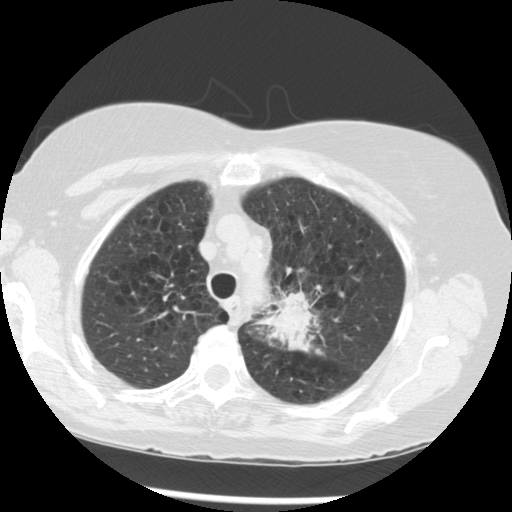
Low-dose screening chest CT, one axial slice; position 223 of 283 along the scan axis; 120 kVp; lung window (W 1500 / L -600 HU); 2.5 mm slice thickness; 512 × 512 image matrix, field of view 330 × 330 mm.
Structures marked on this image (manually delineated by an expert):
- lesion 1 (tumor, upper lobe of left lung): bounding box (x1, y1, x2, y2) in pixels: (251, 291, 322, 353)